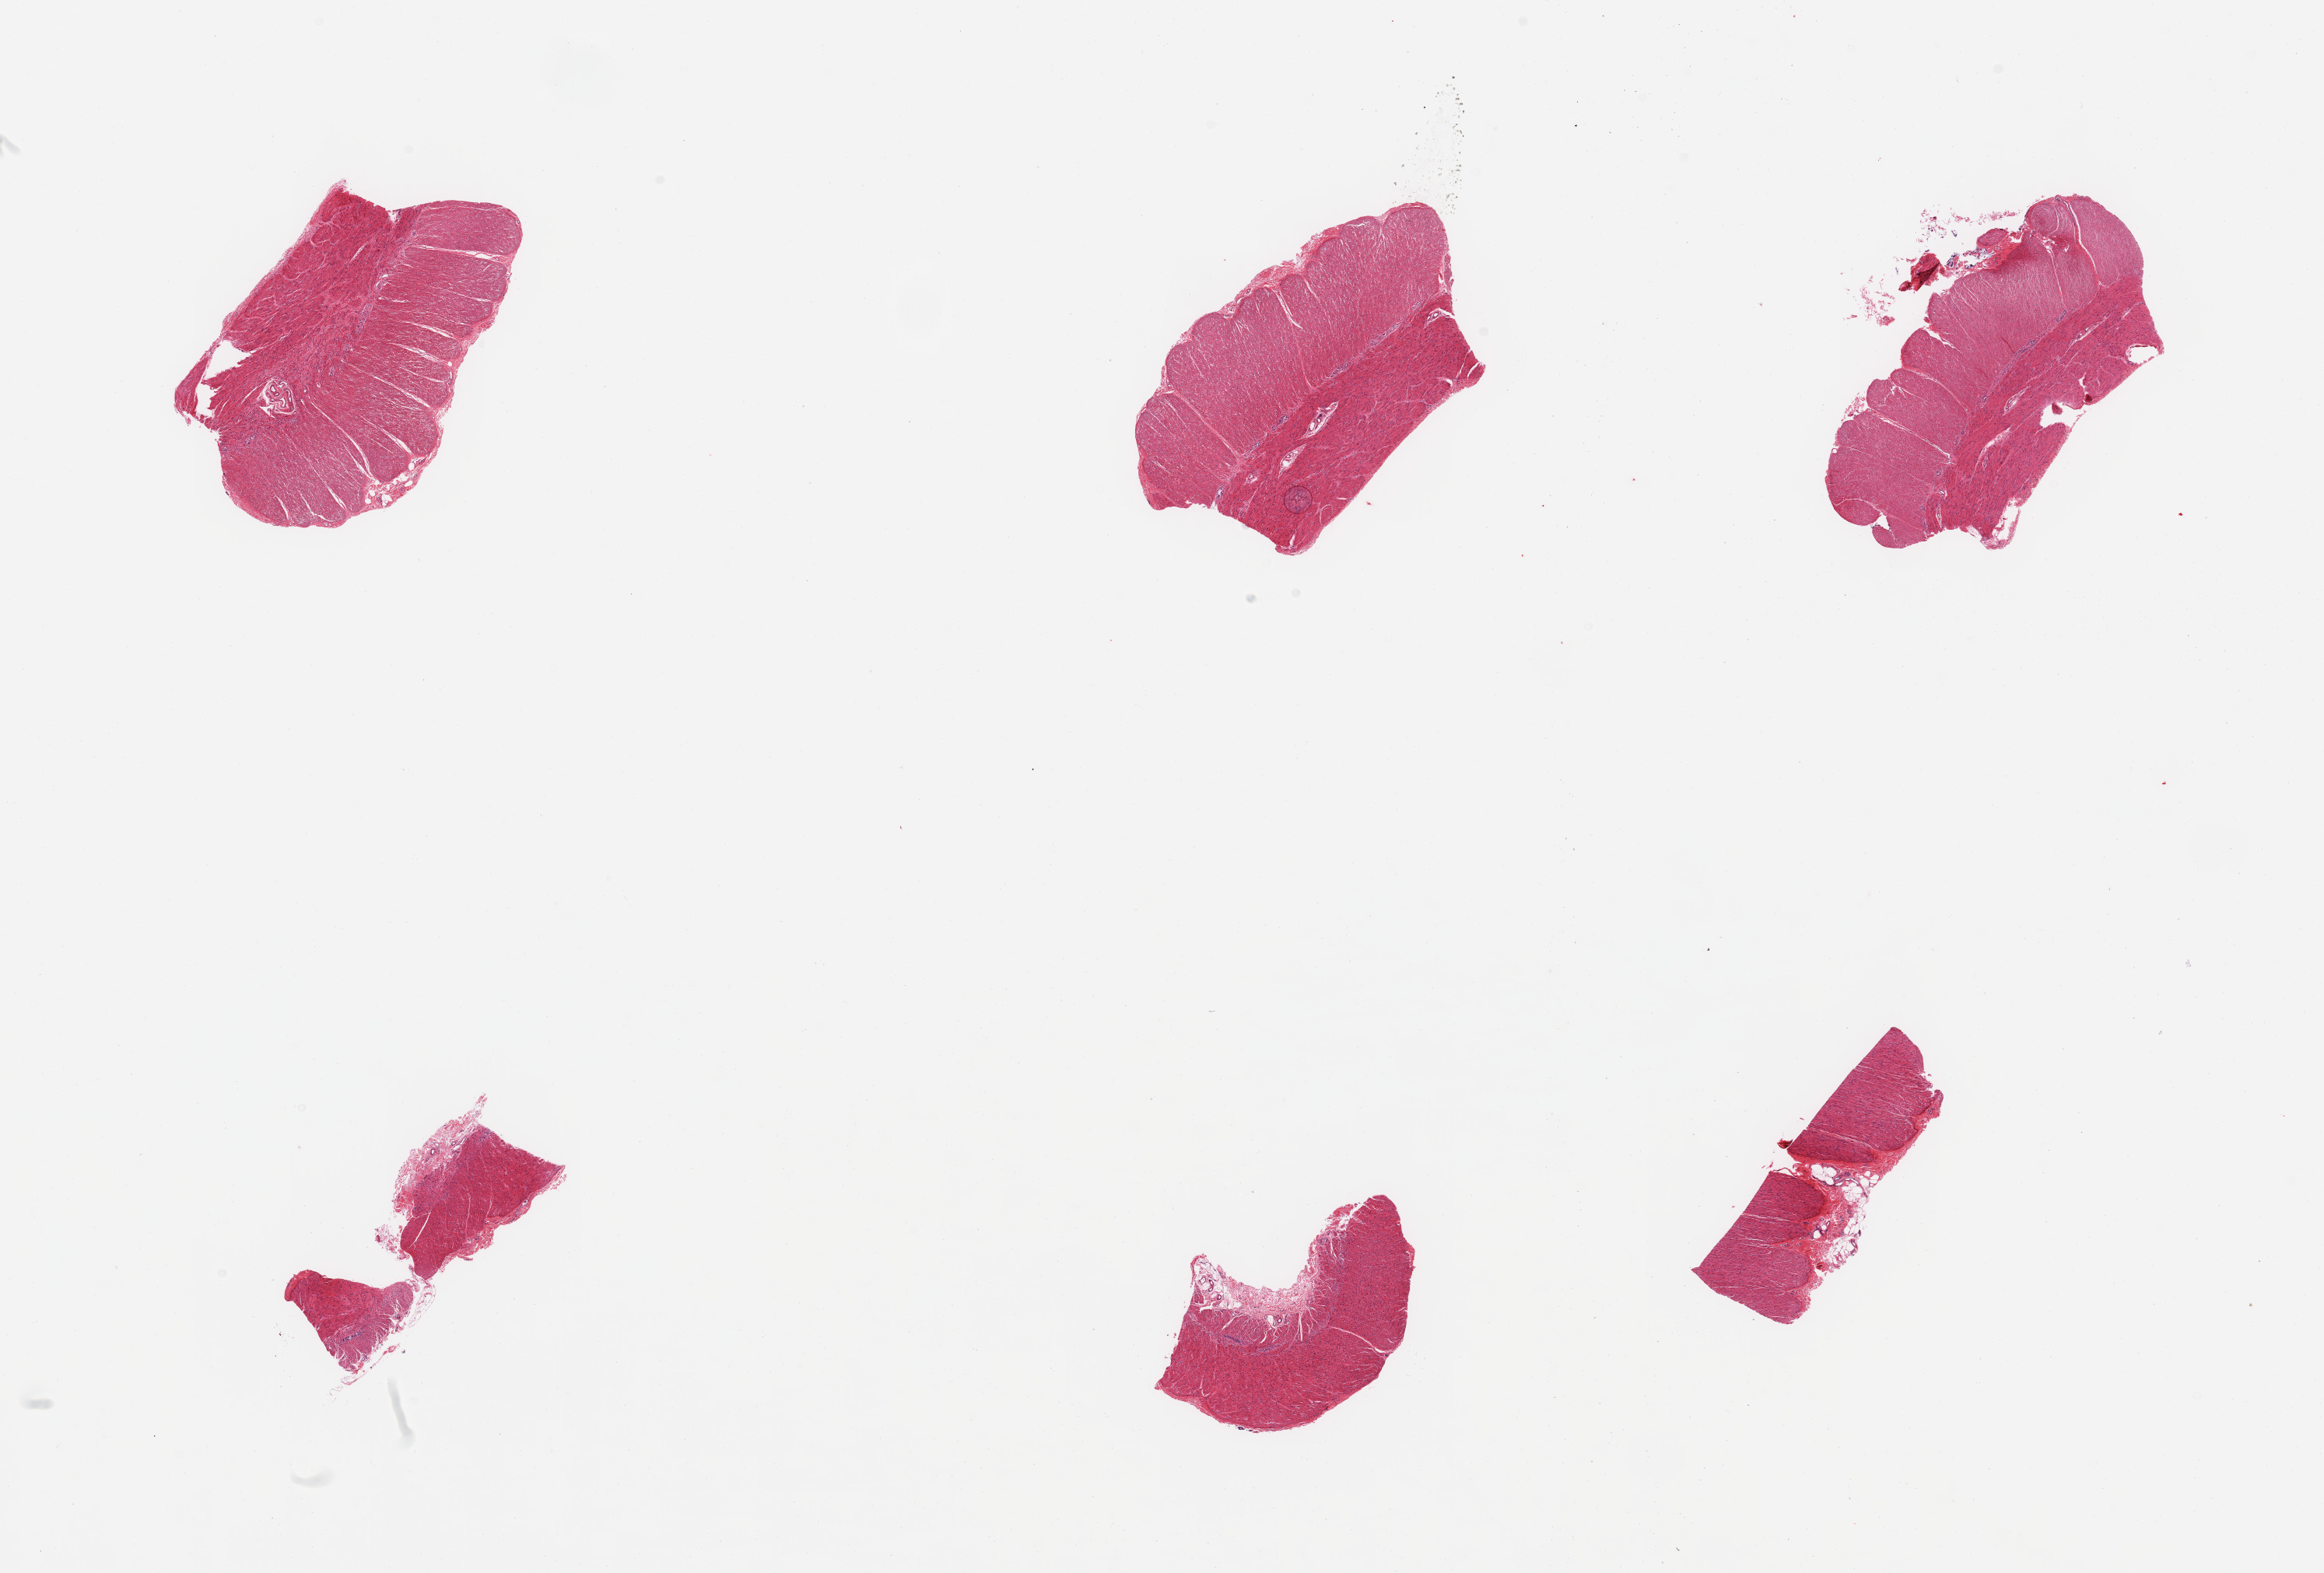
Haematoxylin and eosin whole-slide image, shown as a low-resolution overview of the whole scanned area (about 23.6 x 16.0 mm); PAXgene-fixed paraffin-embedded (PFPE) section; section of sigmoid colon (target tissue); donor tissue sample.
* review note (as recorded): 6 pieces; target muscularis